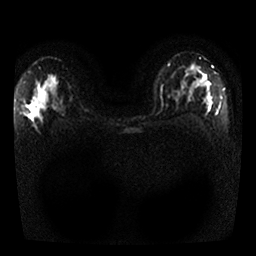
Breast MRI, one axial slice. Slice 17 of 25 in the series (ordered by position). Diffusion-weighted series; image 2 of 4 stored at this slice position (different b-values; order by instance number). 1.5 T. 4 mm slice thickness. 256 × 256 image matrix, field of view 320 × 320 mm. Female patient.
Outlined on this slice (outlined manually by an expert reader):
- tumour on diffusion-weighted imaging: bounding box (x1, y1, x2, y2) in pixels: (198, 72, 210, 88)